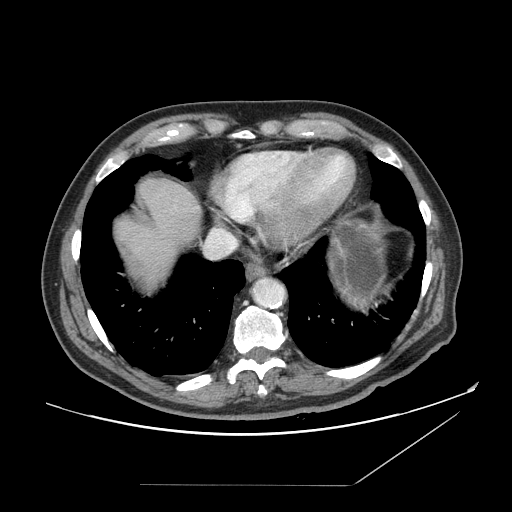
Contrast-enhanced abdominal CT, one axial slice. Position 141 of 166 along the scan axis. 120 kVp. Soft-tissue window (W 400 / L 40 HU). 2.5 mm slice thickness. 512 × 512 image matrix, field of view 416 × 416 mm. Male patient, age 80 years. Case-level facts recorded for this patient, not image findings: diagnosis: colorectal cancer liver metastases, imaged before liver resection; multiple liver metastases: no; largest metastasis: 2.2 cm; chemotherapy before resection: no.
Annotated regions visible in this slice (outlined manually by an expert reader):
- liver: bounding box <113,178,202,294> (left, top, right, bottom; pixels)
- planned liver remnant (the part of the liver to remain after resection): <113,178,202,258>